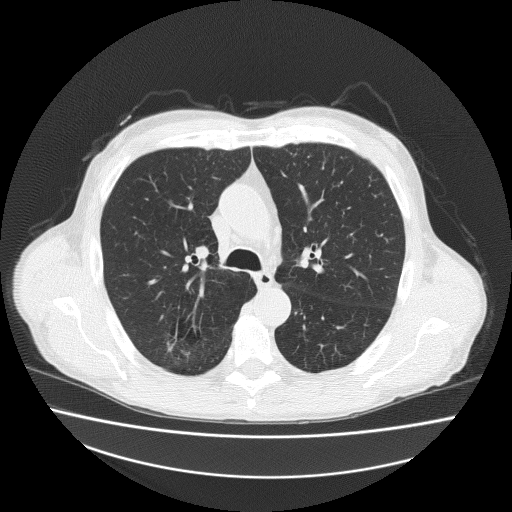
Low-dose screening chest CT, axial slice; second annual screen; lung window (W 1500 / L -600 HU); lung (sharp) reconstruction kernel (FC51); 120 kVp; slice 70 of 186 in the series. Male, age 73 years at enrolment.
Expert-annotated lung lesion, bounding box (x1, y1, x2, y2) in pixels: (159, 314, 214, 358). No non-calcified nodule or mass ≥4 mm was recorded by the screening reader at this exam. Official screen result: negative screen, minor abnormalities not suspicious for lung cancer. Later outcome: lung cancer diagnosed 418 days after this screen — adenosquamous carcinoma, right upper lobe, well differentiated (G1), stage IA (AJCC 6th edition), 20 mm at pathology.